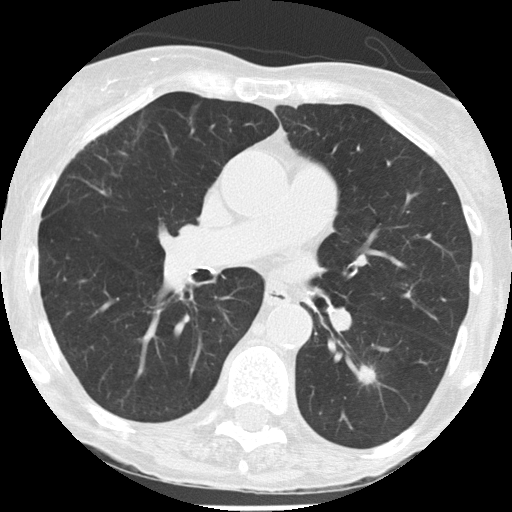
Low-dose screening chest CT, axial slice; third annual screen; lung window (W 1500 / L -600 HU); lung (sharp) reconstruction kernel (FC51). Female, age 68 years at enrolment. Former smoker at enrolment.
Expert reader's lesion annotation, box from (x=336, y=348) to (x=398, y=404) px. Reader record for this screening exam (exam-level; its link to the box is not recorded): non-calcified nodule or mass ≥4 mm, left lower lobe, 11 × 9 mm, spiculated (stellate) margins, soft tissue attenuation, pre-existing on the prior screen: yes; interval growth: yes. Official screen result: positive, other.